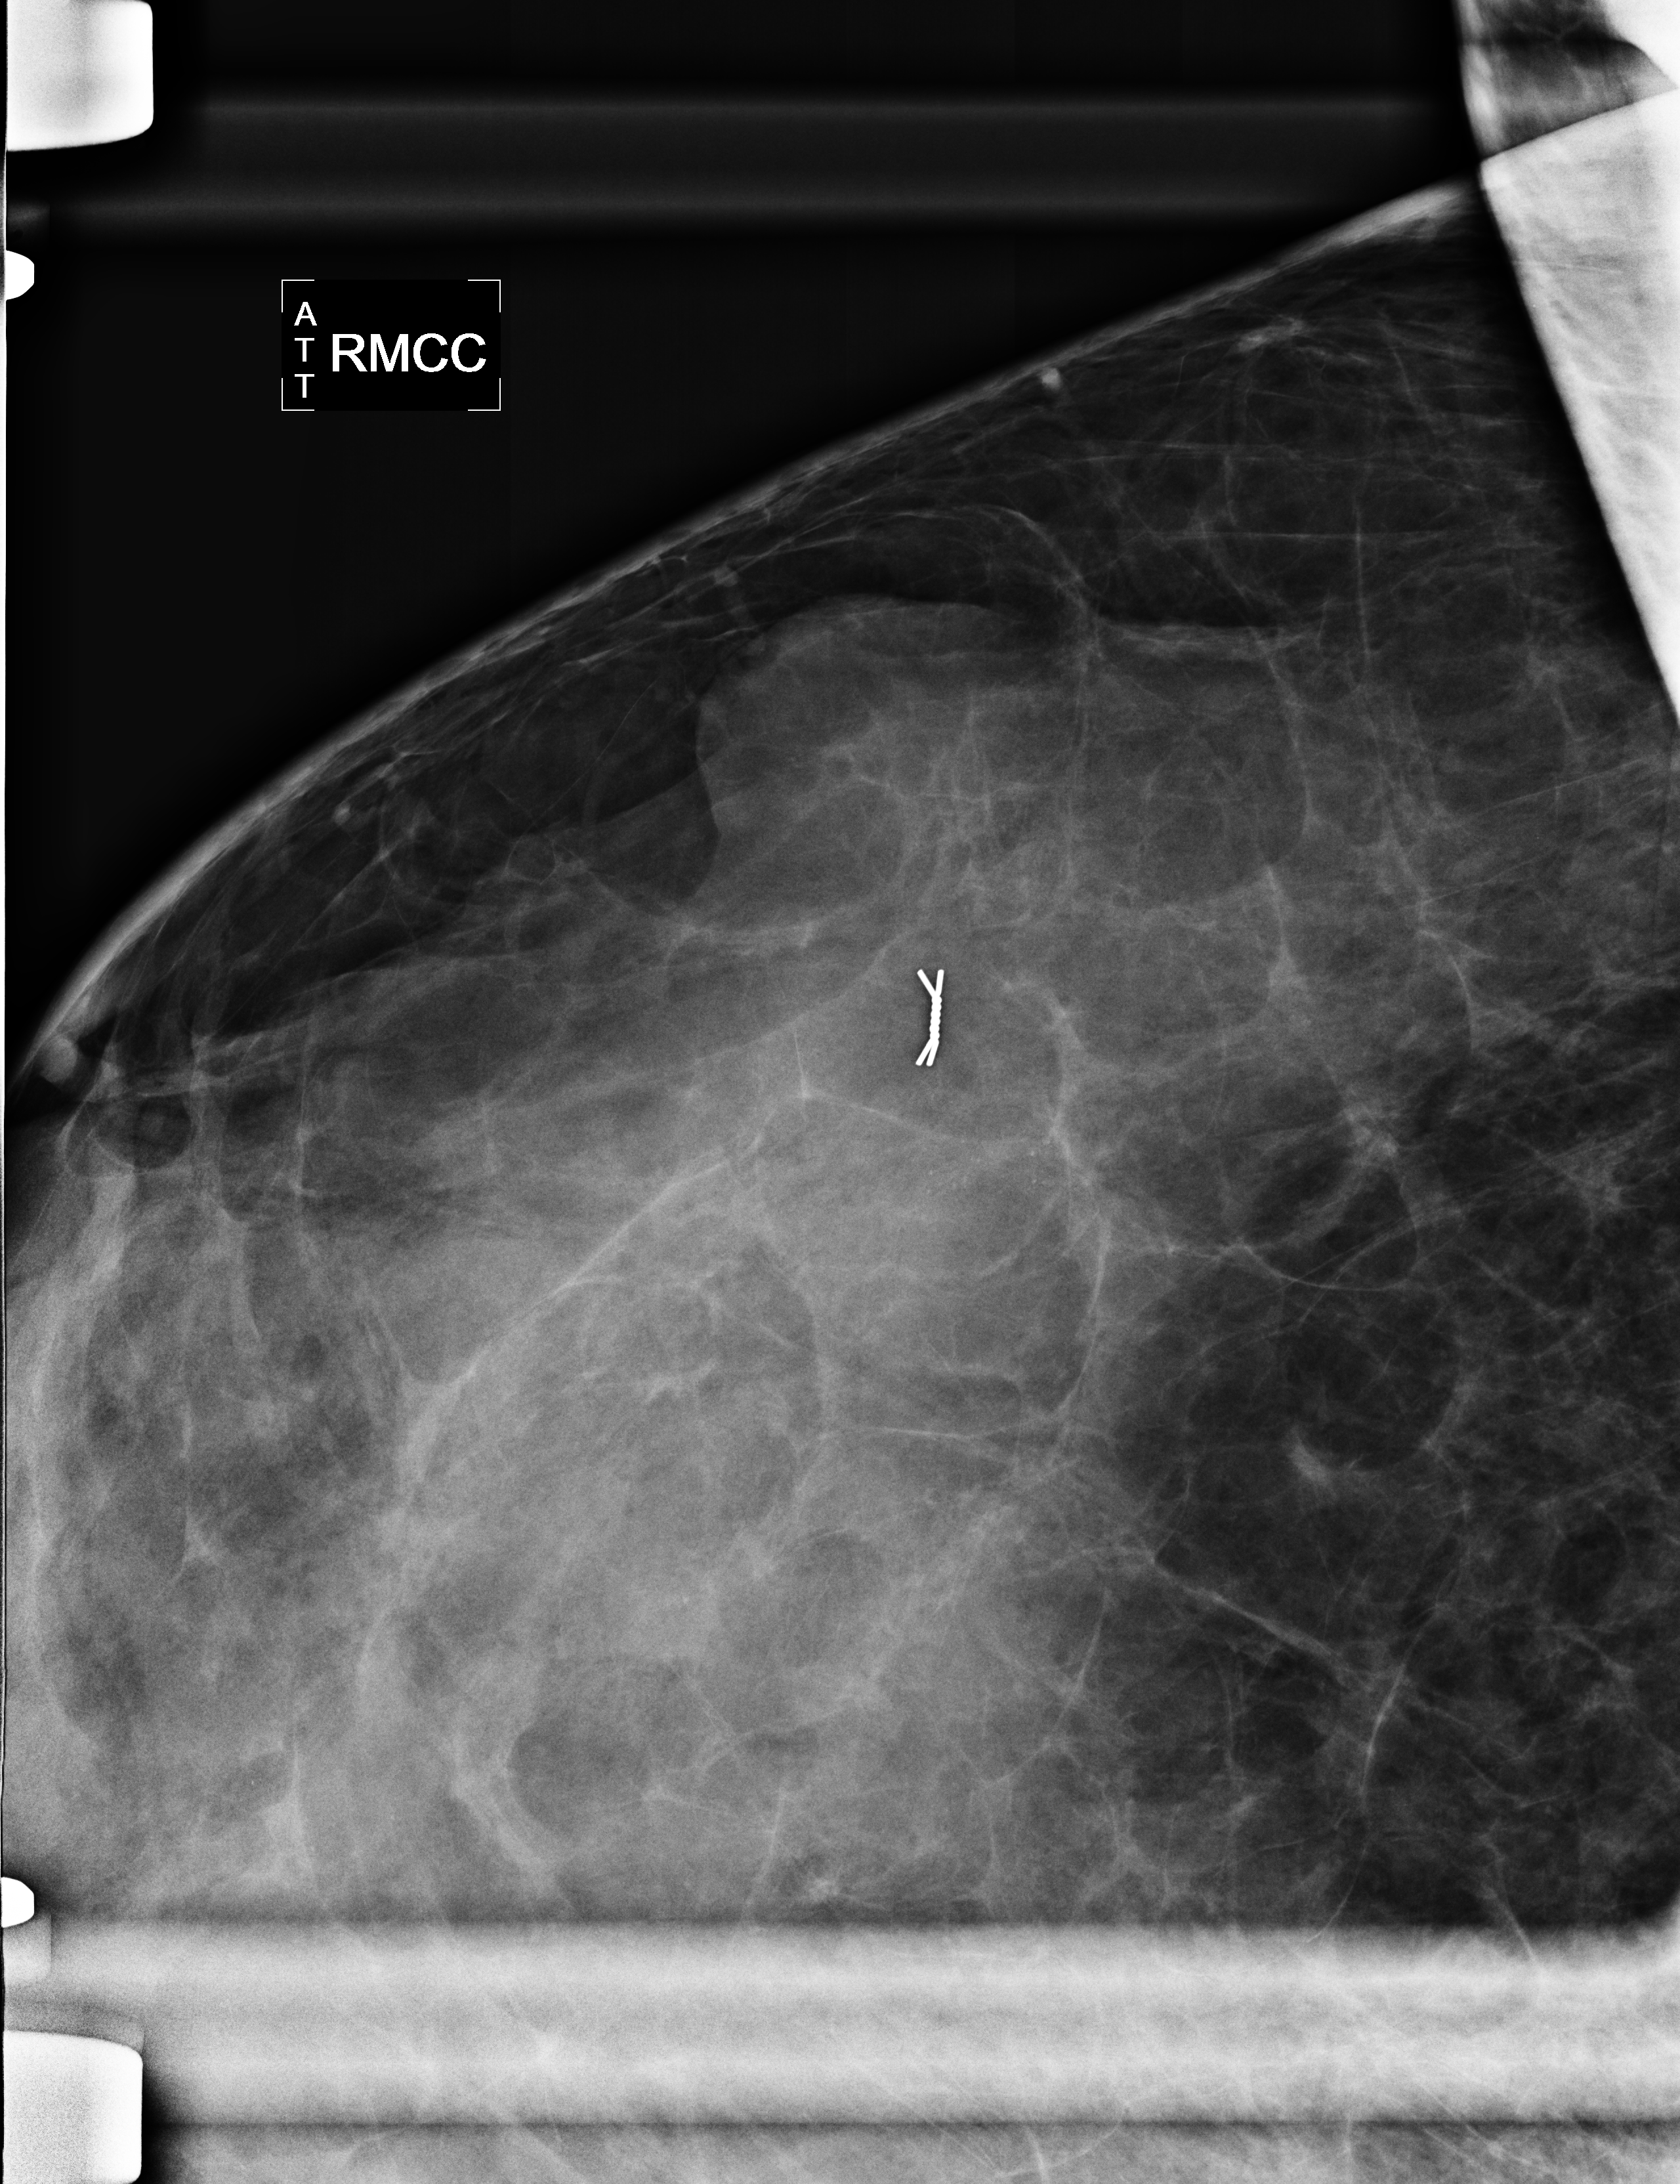
Mammogram, right breast, CC view.
Patient-level pathology facts (clinical record, not image findings): pathology diagnosis: benign fibroadenoma (right breast); pathology report notes: RIGHT BREAST CALCIFICATION WITH NEEDLE LOCATION: FIBROADENOMA (1.9CM). REMAINING BREAST TISSUE WITH ADENOSIS, FOCAL FIBROADENOMATOUS CHANGES, APOCRINE METAPLASIA, FIBROCYSTIC CHANGES, SMALL INTRADUCTAL PAPILLOMAS, AND USUAL TYPE DUCTAL HYPERPLASIA. MICROCALCIFICATIONS ASSOCIATED WITH BENIGN BREAST TISSUE ARE IDENTIFIED. NO IN-SITU OR INVASIVE CARCINOMA.